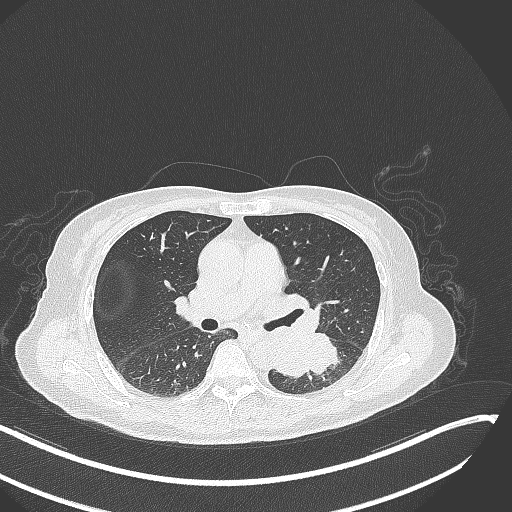
Chest CT, one axial slice; reconstruction kernel B70f; 120 kVp; lung window (W 1500 / L -600 HU); 1 mm slice thickness; 512 × 512 image matrix, field of view 400 × 400 mm. Female patient, age 64 years. Case-level facts recorded for this patient, not image findings: clinical TNM (as recorded): T3 N1 M1; histopathological grade: G3.
Outlined on this slice (rectangle marked by the reading radiologist):
- lung tumour (recorded histology: small cell carcinoma): box from (x=273, y=323) to (x=343, y=383) px